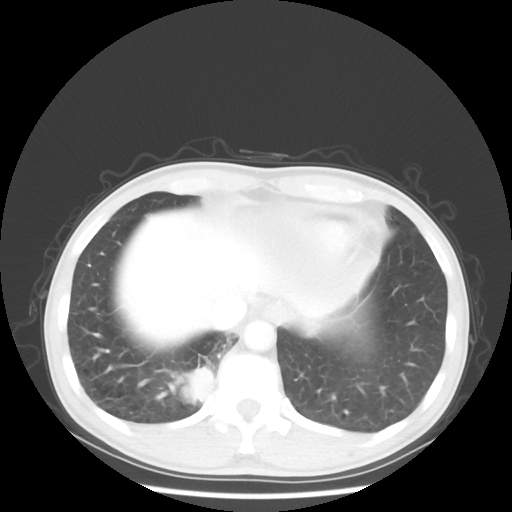
Chest CT, one axial slice; slice 9 of 58 in the series (ordered by position); reconstruction kernel STANDARD; 100 kVp; lung window (W 1500 / L -600 HU); 5 mm slice thickness; 512 × 512 image matrix. Male patient, age 56 years. Case-level facts recorded for this patient, not image findings: clinical TNM (as recorded): T2 N1 M1; histopathological grade: G1.
Annotated regions visible in this slice (bounding box drawn by a radiologist):
- lung tumour (recorded histology: adenocarcinoma): bounding box (x1, y1, x2, y2) in pixels: (180, 362, 216, 406)